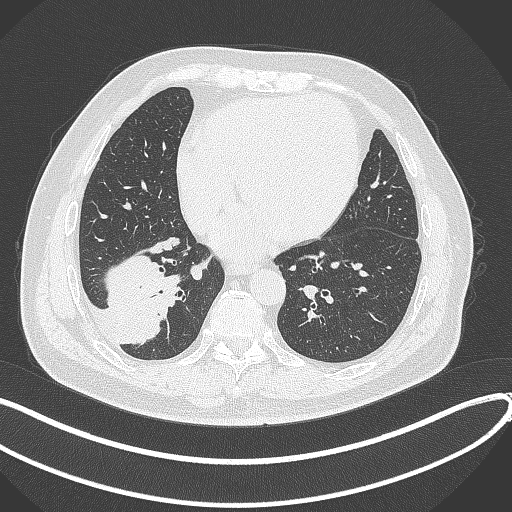
Chest CT, one axial slice. Slice 125 of 360 in the series (ordered by position). Reconstruction kernel B70f. Lung window (W 1500 / L -600 HU). 512 × 512 image matrix, field of view 400 × 400 mm. Male patient, age 59 years.
Outlined on this slice (bounding box drawn by a radiologist):
- lung tumour (recorded histology: adenocarcinoma): box from (x=103, y=256) to (x=189, y=347) px